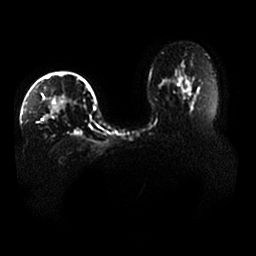
Breast MRI, one axial slice; slice 29 of 33 in the series (ordered by position); diffusion-weighted series; image 2 of 4 stored at this slice position (different b-values; order by instance number); 1.5 T; 4 mm slice thickness; 256 × 256 image matrix, field of view 400 × 400 mm. Female patient.
Outlined on this slice (manually delineated by an expert):
- tumour on diffusion-weighted imaging: box from (x=42, y=97) to (x=67, y=120) px